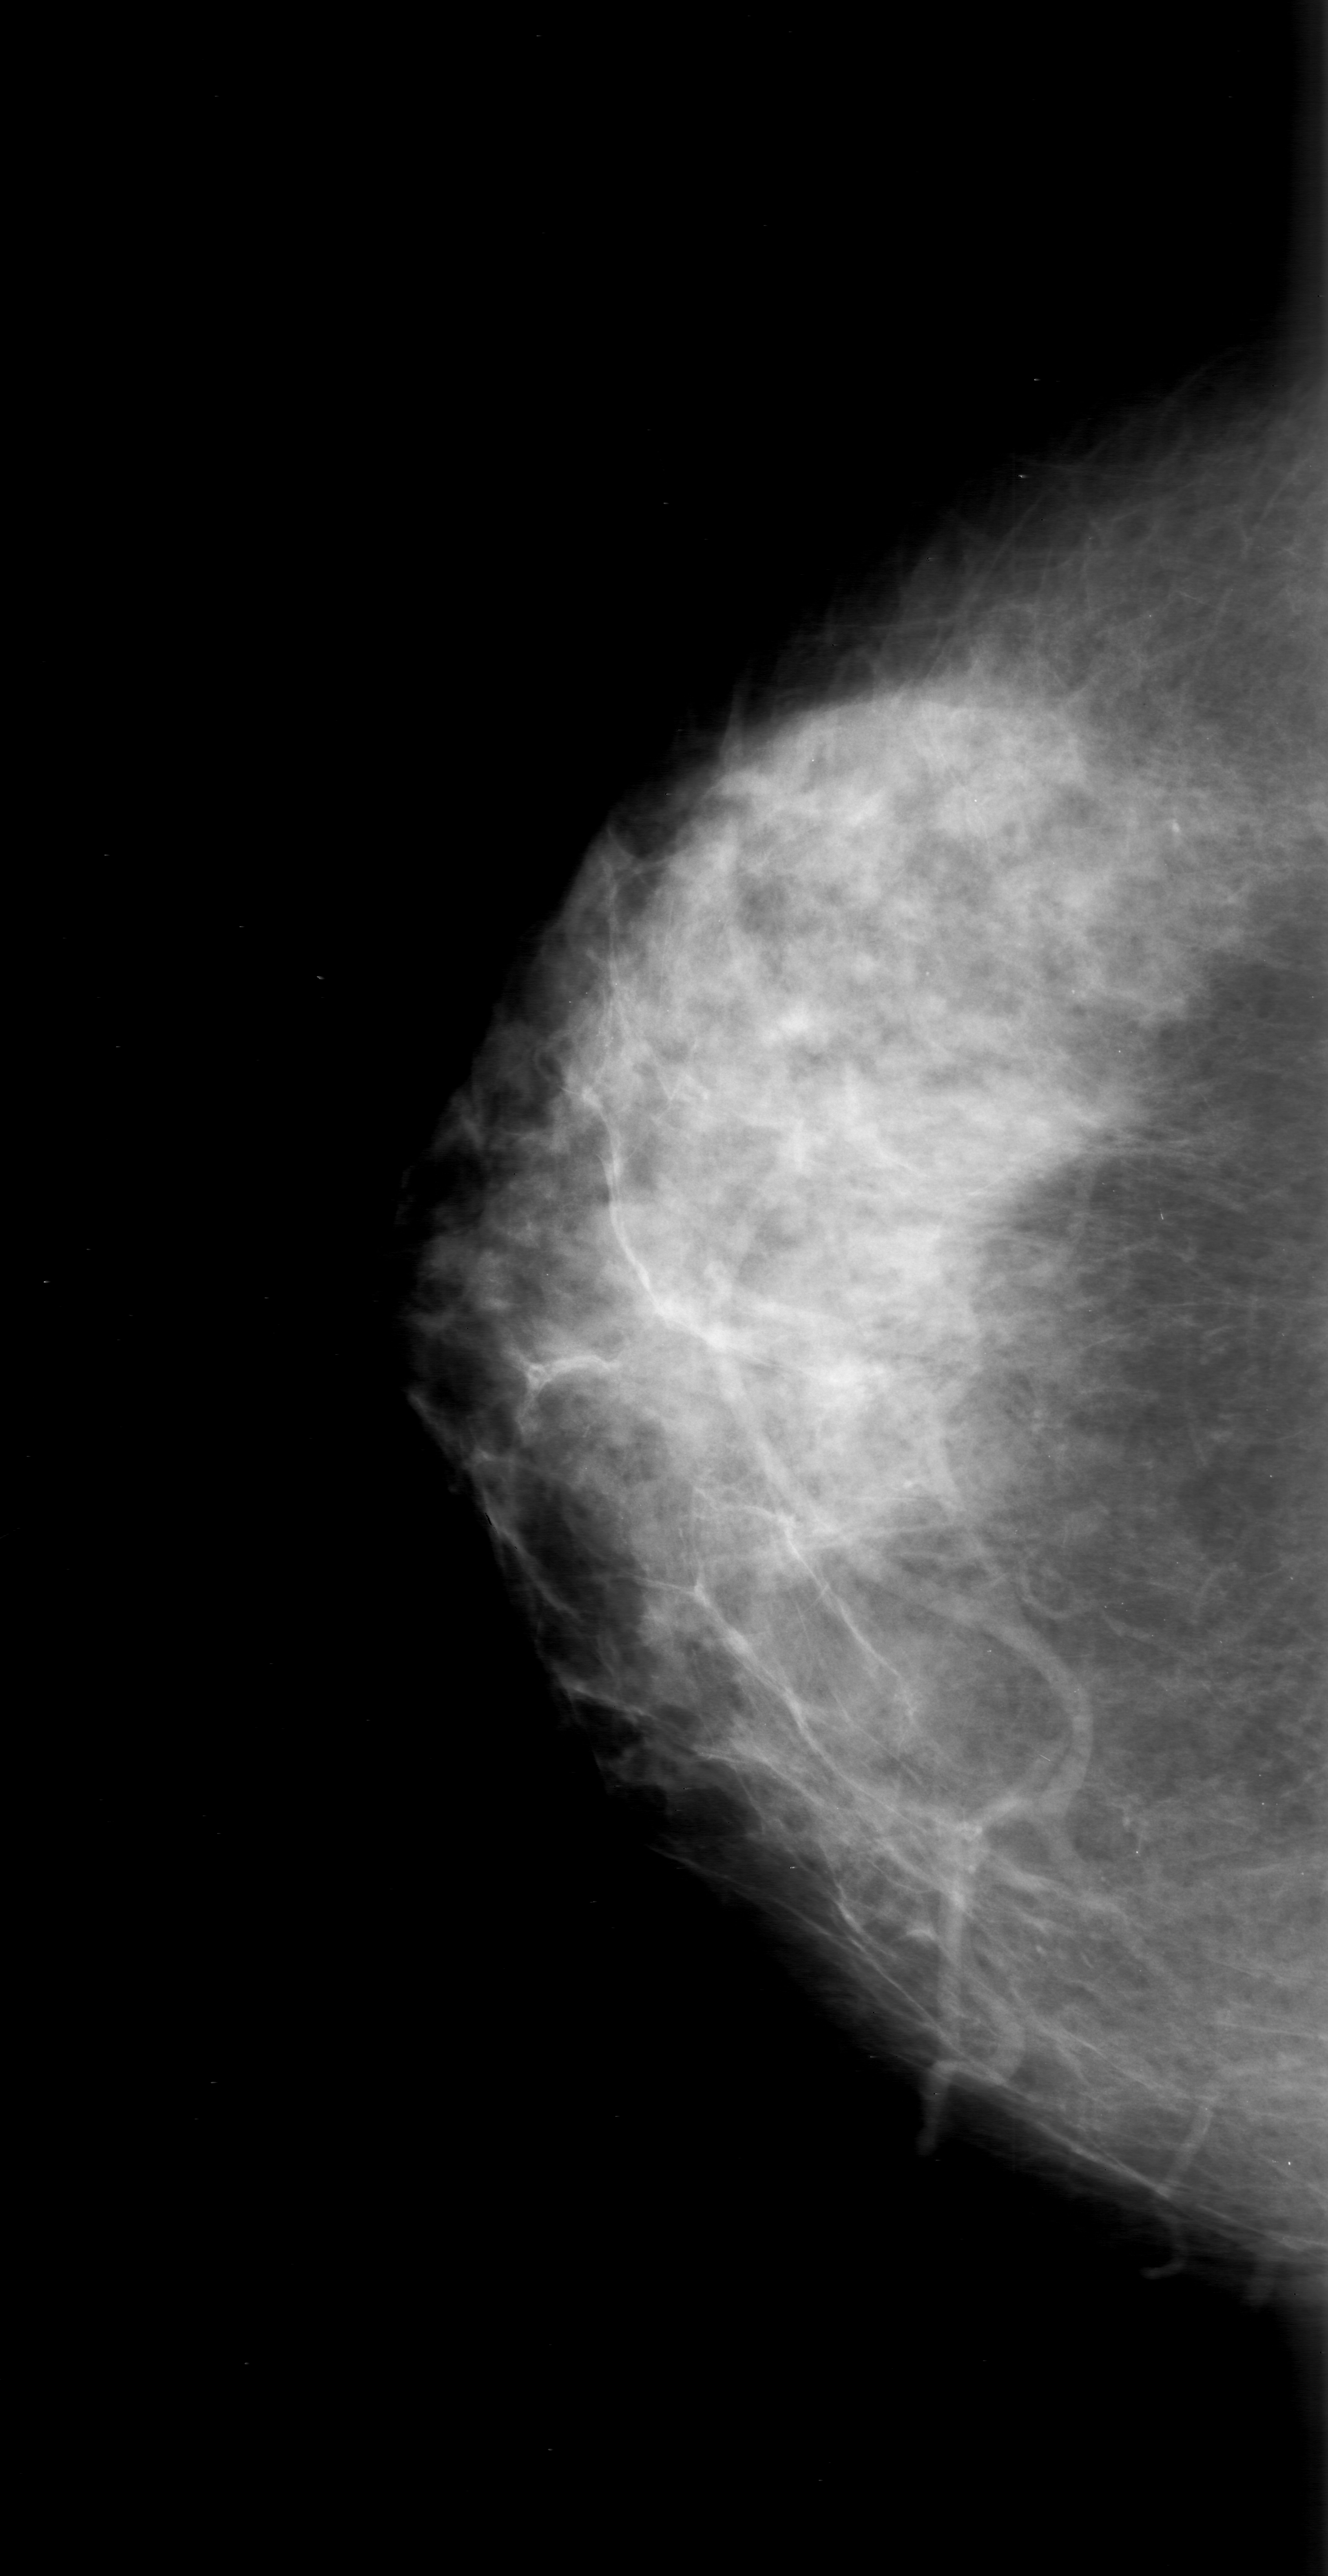
Scanned film-screen mammogram. Right breast. CC view. 1328 × 2576 image matrix.
Marked abnormalities (boxes around the expert regions of interest):
- calcifications, morphology punctate, distribution clustered; BI-RADS assessment category 0 (incomplete: needs additional imaging); subtlety rating 1 on a 1 (subtle) to 5 (obvious) scale; pathology result (as recorded, not read from the image): benign: bounding box <513,943,707,1147> (left, top, right, bottom; pixels)